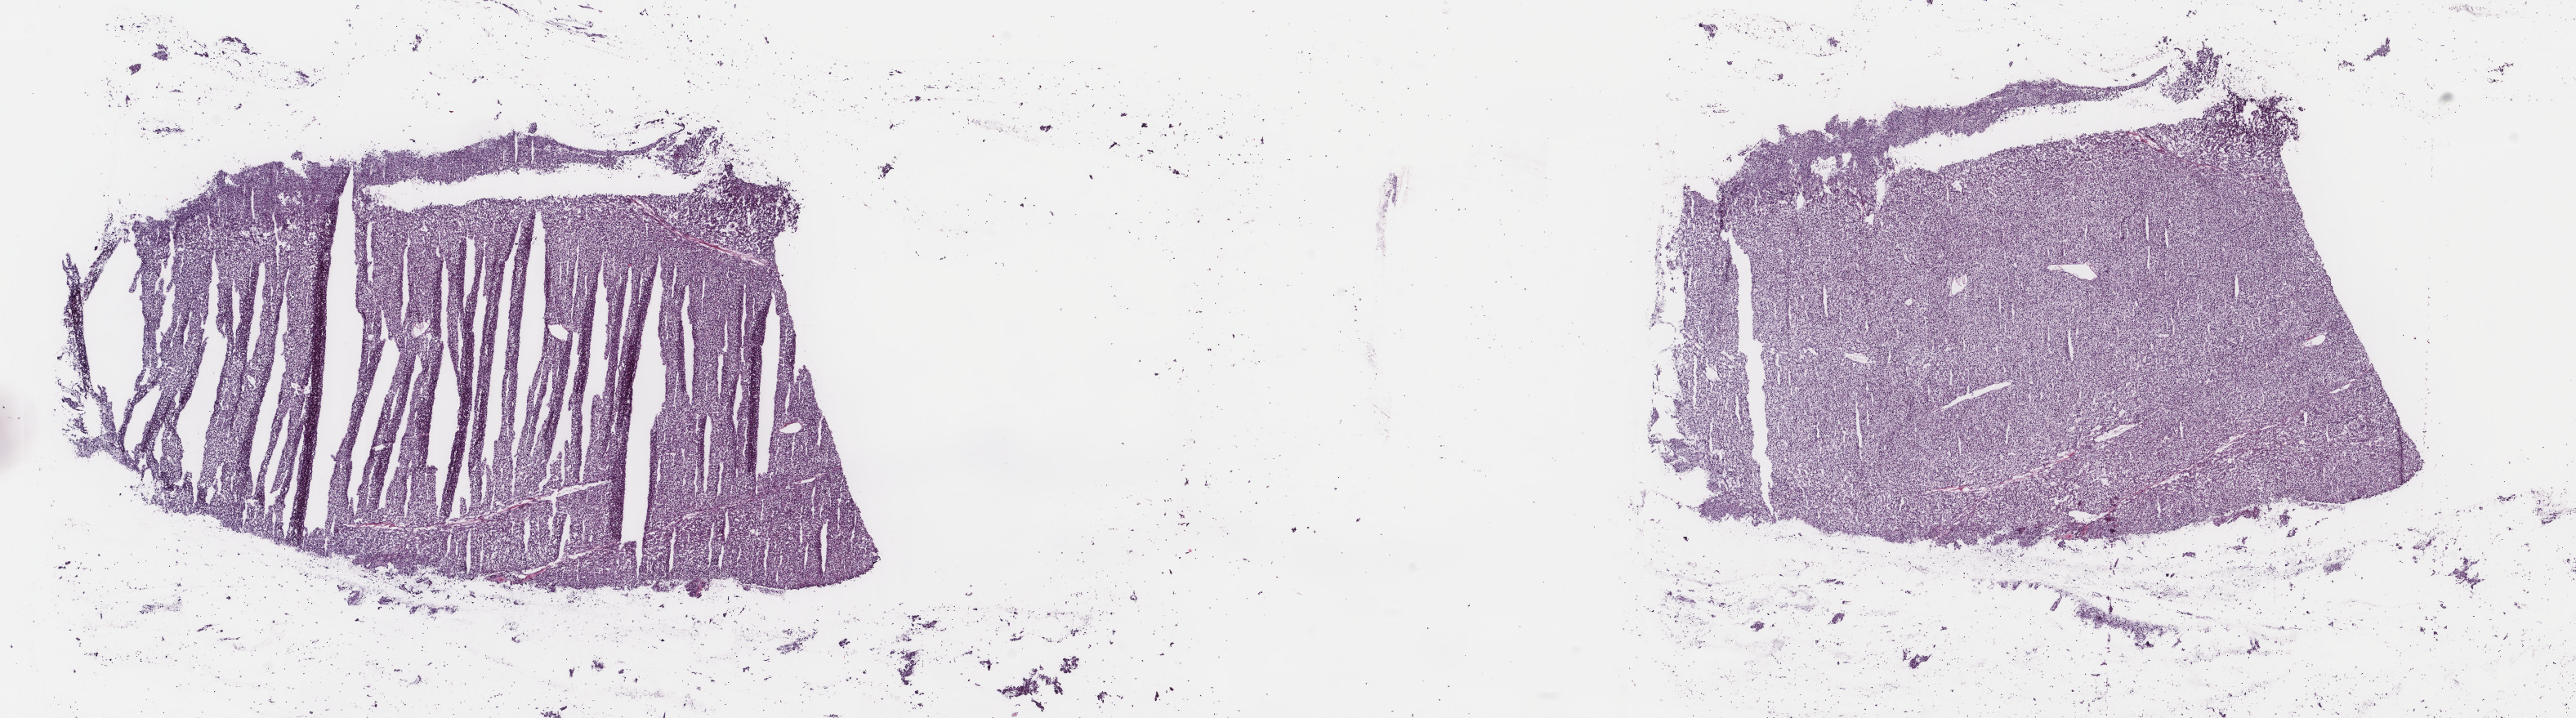
Digitized H&E-stained tissue section (whole slide) — whole scanned area (about 25.0 x 7.0 mm, from a 40x scan) shown as a low-resolution overview; frozen section from the top of the tissue portion; sample: primary tumour, liver. Patient: female, age at initial diagnosis 63 years. Histologic grade: G3 (poorly differentiated). Slide review estimates, as recorded: tumour cells 100%, tumour nuclei 95%, normal cells 0%, stromal cells 0%, necrosis 0%. Infiltration values recorded for this section: lymphocyte infiltration 0%, monocyte infiltration 0%, neutrophil infiltration 0%.
AJCC pathologic stage: I. Histologic diagnosis: Hepatocellular carcinoma, NOS. TNM: T1 N0 M0.